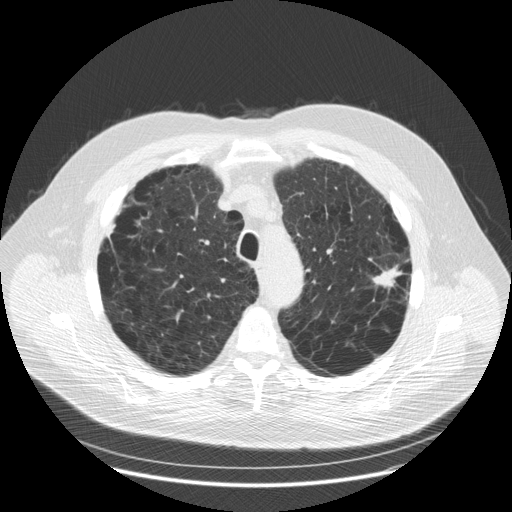
Low-dose screening chest CT, axial slice, baseline screening round, lung window (W 1500 / L -600 HU), 2.5 mm slice thickness, slice 43 of 179 in the series, 512 × 512 image matrix. Male participant, aged 70 years at enrolment. Current smoker at enrolment.
Expert reader's lesion annotation, bounding box [x1, y1, x2, y2] px = [363, 249, 417, 300]. Screening reader's record for this exam (one nodule recorded; not confirmed to be the boxed lesion): non-calcified nodule or mass ≥4 mm, left upper lobe, 25 × 13 mm, spiculated (stellate) margins, soft tissue attenuation. Lung cancer was diagnosed 62 days after this screen: adenocarcinoma, NOS, left upper lobe, moderately differentiated (G2), stage IA (AJCC 6th edition), 22 mm at pathology.